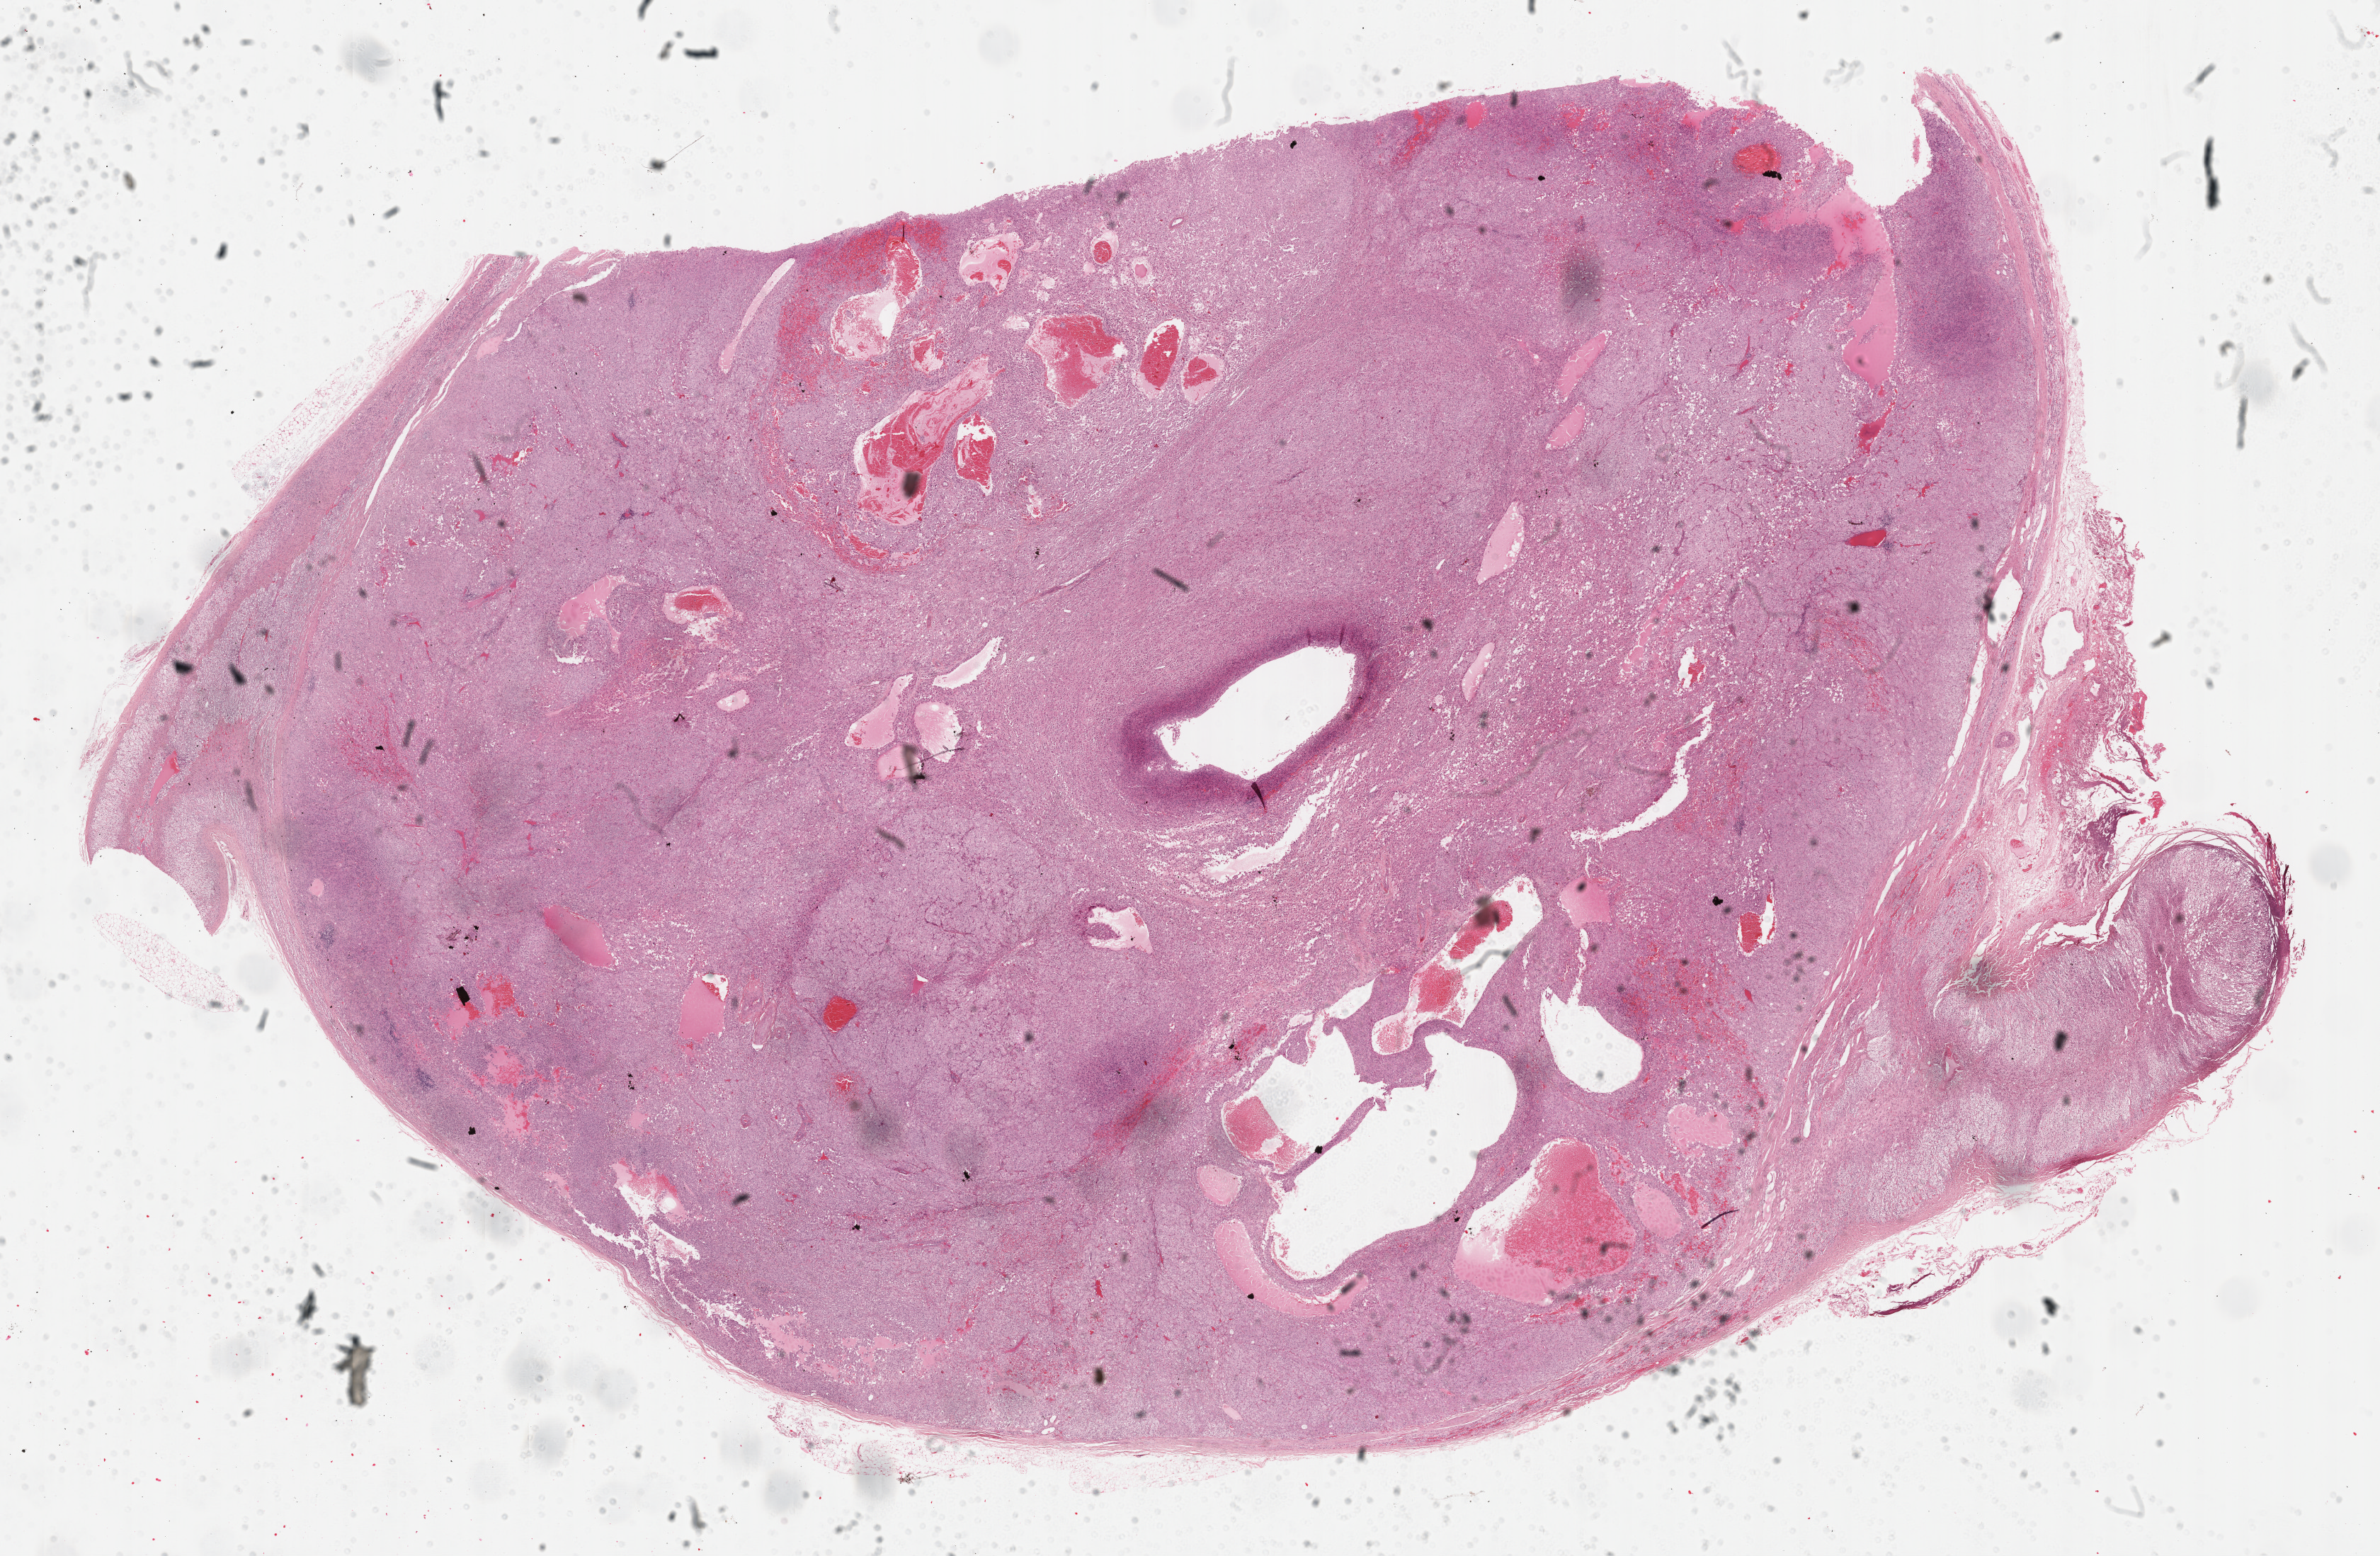
H&E whole-slide image, whole scanned area (about 27.2 x 17.8 mm) shown as a low-resolution overview. Formalin-fixed paraffin-embedded (FFPE) diagnostic section. Adrenal cortex, primary tumour sample. Patient: male, age at initial diagnosis 22 years.
Pathologic diagnosis: Adrenal cortical carcinoma (cortex of adrenal gland).